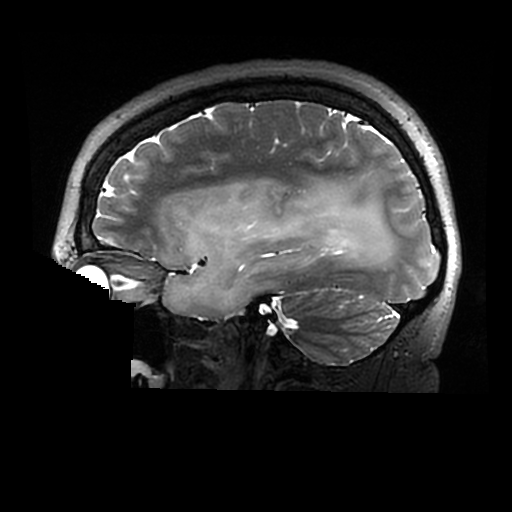
Brain MRI from a brain-tumour surgery series, one sagittal slice; position 202 of 320 along the scan axis; 0.6 mm slice thickness; 512 × 512 image matrix. From the clinical record (not read from this slice): histopathology: Astrocytoma; WHO grade: 2; IDH mutation: yes.
Structures marked on this image (manually delineated by an expert):
- tumour: bounding box <162,180,395,318> (left, top, right, bottom; pixels)